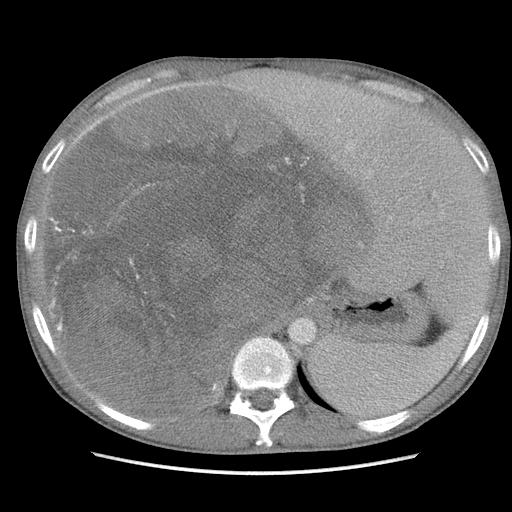
Contrast-enhanced abdominal CT, one axial slice; position 80 of 115 along the scan axis; soft-tissue window (W 400 / L 40 HU); 5 mm slice thickness; 512 × 512 image matrix, field of view 360 × 360 mm. Male patient. From the clinical record (not read from this slice): diagnosis: adrenocortical carcinoma; tumour side: right adrenal; Ki-67 index: 13 %; stage (as recorded): 3.
Structures marked on this image (semi-automatically segmented with operator editing):
- mass: box from (x=49, y=94) to (x=365, y=403) px